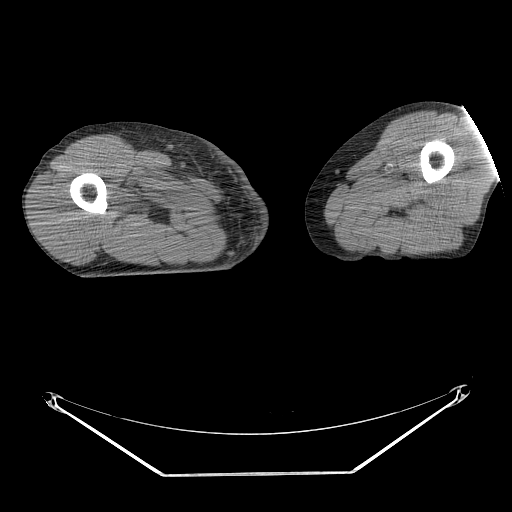
CT of an extremity soft-tissue mass (from a PET/CT study), one axial slice; position 233 of 311 along the scan axis; soft-tissue window (W 400 / L 40 HU); 512 × 512 image matrix, field of view 500 × 500 mm. Male patient. From the clinical record (not read from this slice): histological type: undifferentiated - pleiomorphic; grade: high; site of the primary tumour: right thigh.
Structures marked on this image (expert contour drawn on MRI and transferred to this co-registered scan by the dataset authors):
- gross tumour volume including surrounding oedema: box from (x=137, y=192) to (x=161, y=216) px